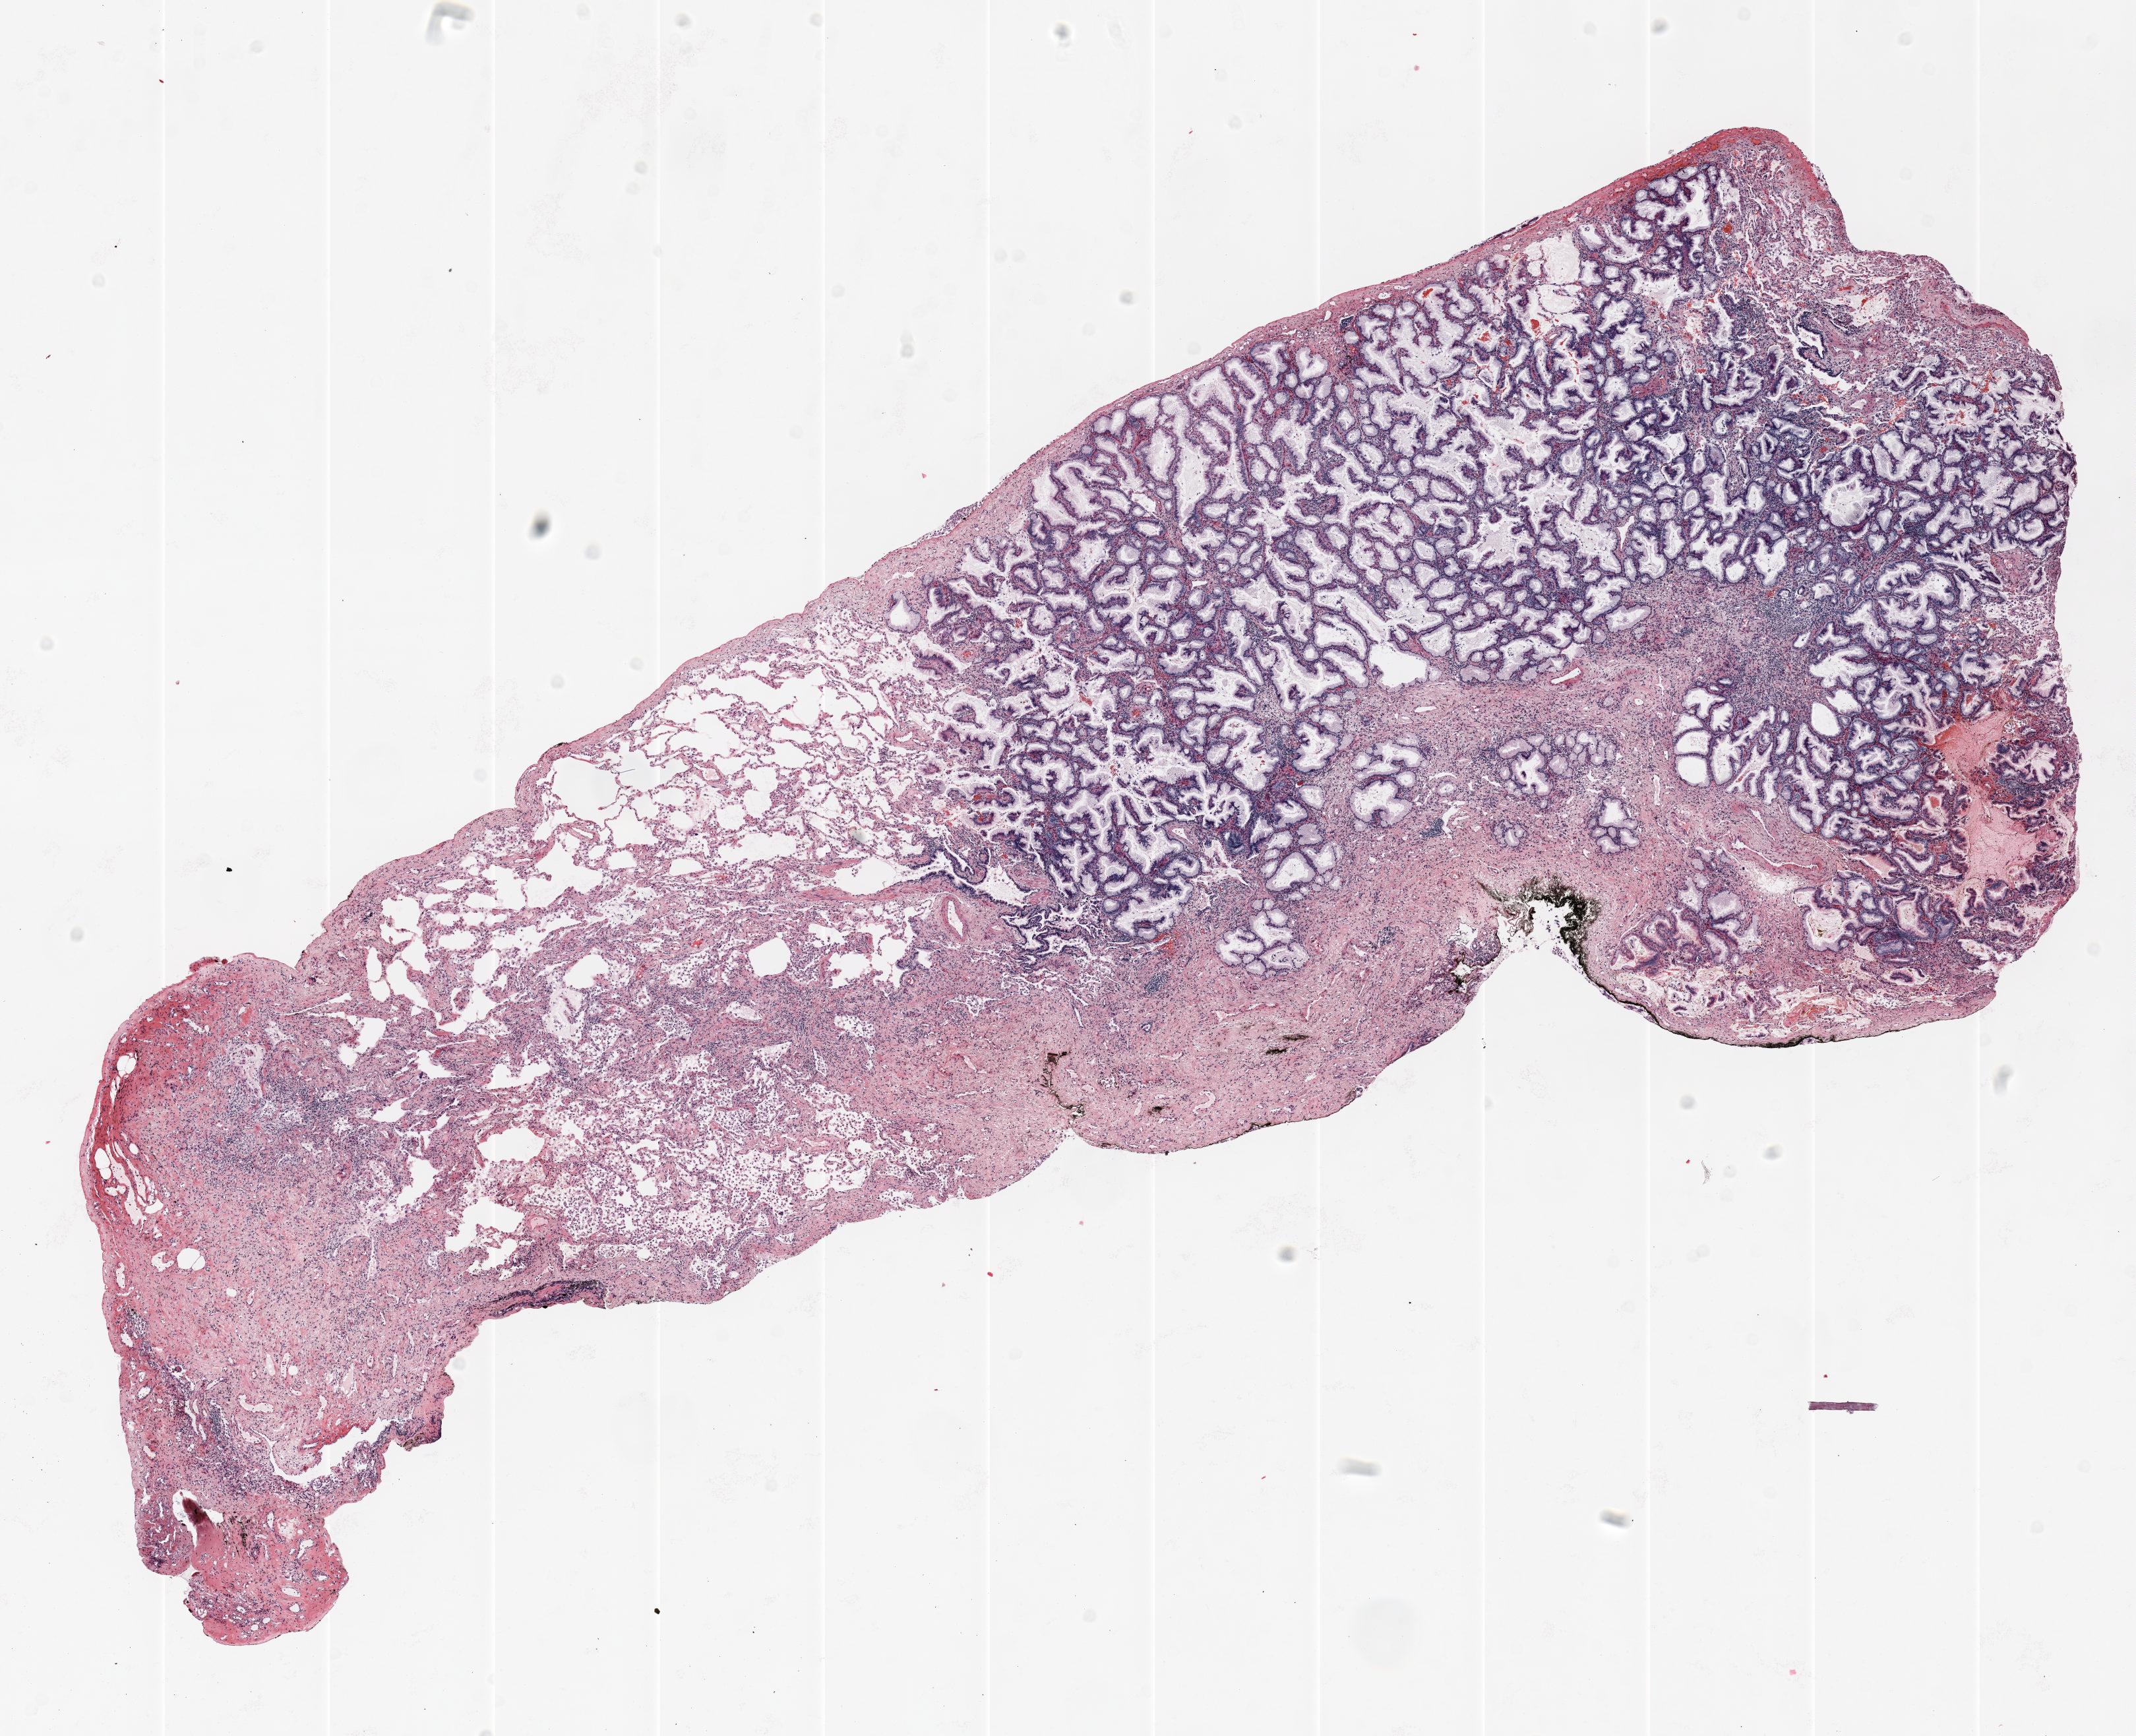
Whole-slide histology image, H&E — low-resolution overview of the scanned area, about 13.0 x 10.6 mm (from a 20x scan), formalin-fixed paraffin-embedded (FFPE) section, lung tissue. Female patient, aged 64 at enrolment. Former smoker at enrolment. Grade: well differentiated (G1).
Participant's lung-cancer diagnosis: Bronchiolo-alveolar adenocarcinoma, NOS. Primary tumour location (clinical record): left lower lobe. ICD-O-3 topography: lower lobe of lung (C34.3). Stage (AJCC 6th edition): IA. Tumour size (pathology): 8 mm.